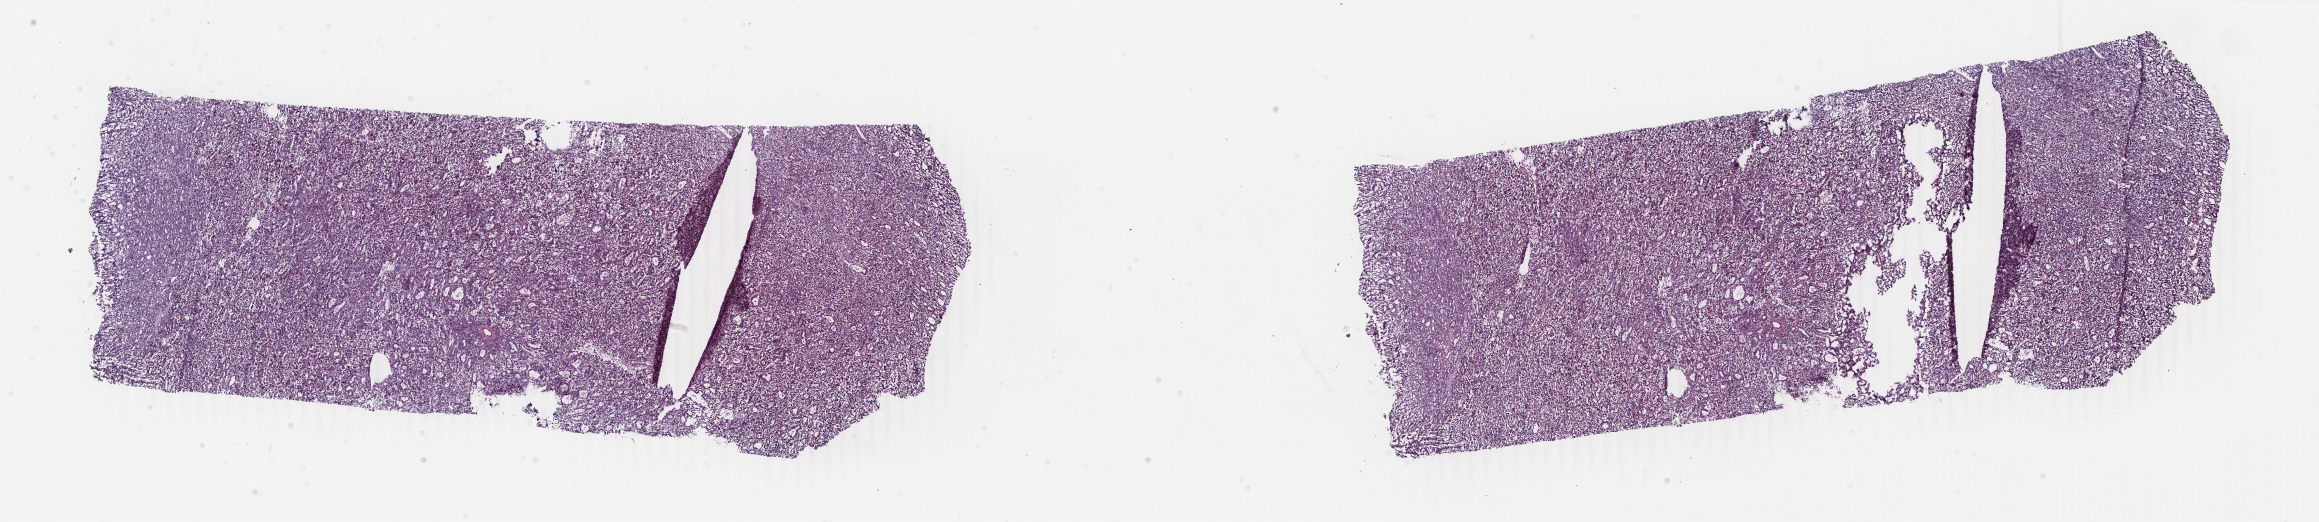
Whole-slide histology image, H&E — a low-resolution overview of the entire scanned area, about 36.9 x 8.3 mm (from a 40x scan), frozen section from the top of the tissue portion, uterus, primary tumour sample. Patient: female, age at initial diagnosis 64 years. Histologic grade: G2 (moderately differentiated). Slide review estimates, as recorded: tumour cells 96%, tumour nuclei 85%, normal cells 0%, stromal cells 3%, necrosis 1%. Infiltration values recorded for this section: lymphocyte infiltration 6%, monocyte infiltration 3%, neutrophil infiltration 0%.
FIGO stage: IA. Pathologic diagnosis: Endometrioid adenocarcinoma, NOS (endometrium).